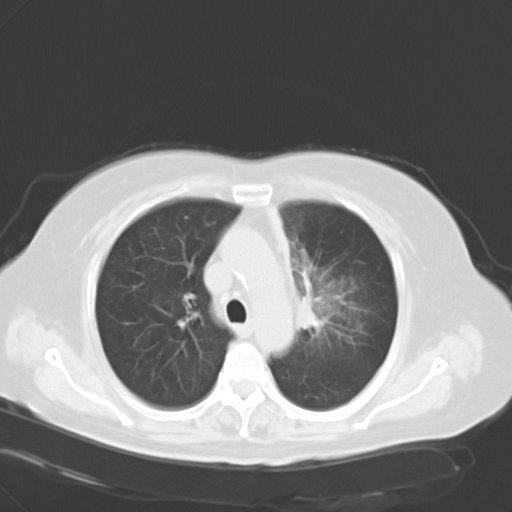
Chest CT, one axial slice. Slice 20 of 28 in the series (ordered by position). 120 kVp. Lung window (W 1500 / L -600 HU). 512 × 512 image matrix, field of view 353 × 353 mm. Patient: female, 65 years. Case-level facts recorded for this patient, not image findings: clinical TNM (as recorded): T2b N1 M0.
Annotated regions visible in this slice (rectangle marked by the reading radiologist):
- lung tumour (recorded histology: adenocarcinoma): box from (x=294, y=285) to (x=328, y=339) px